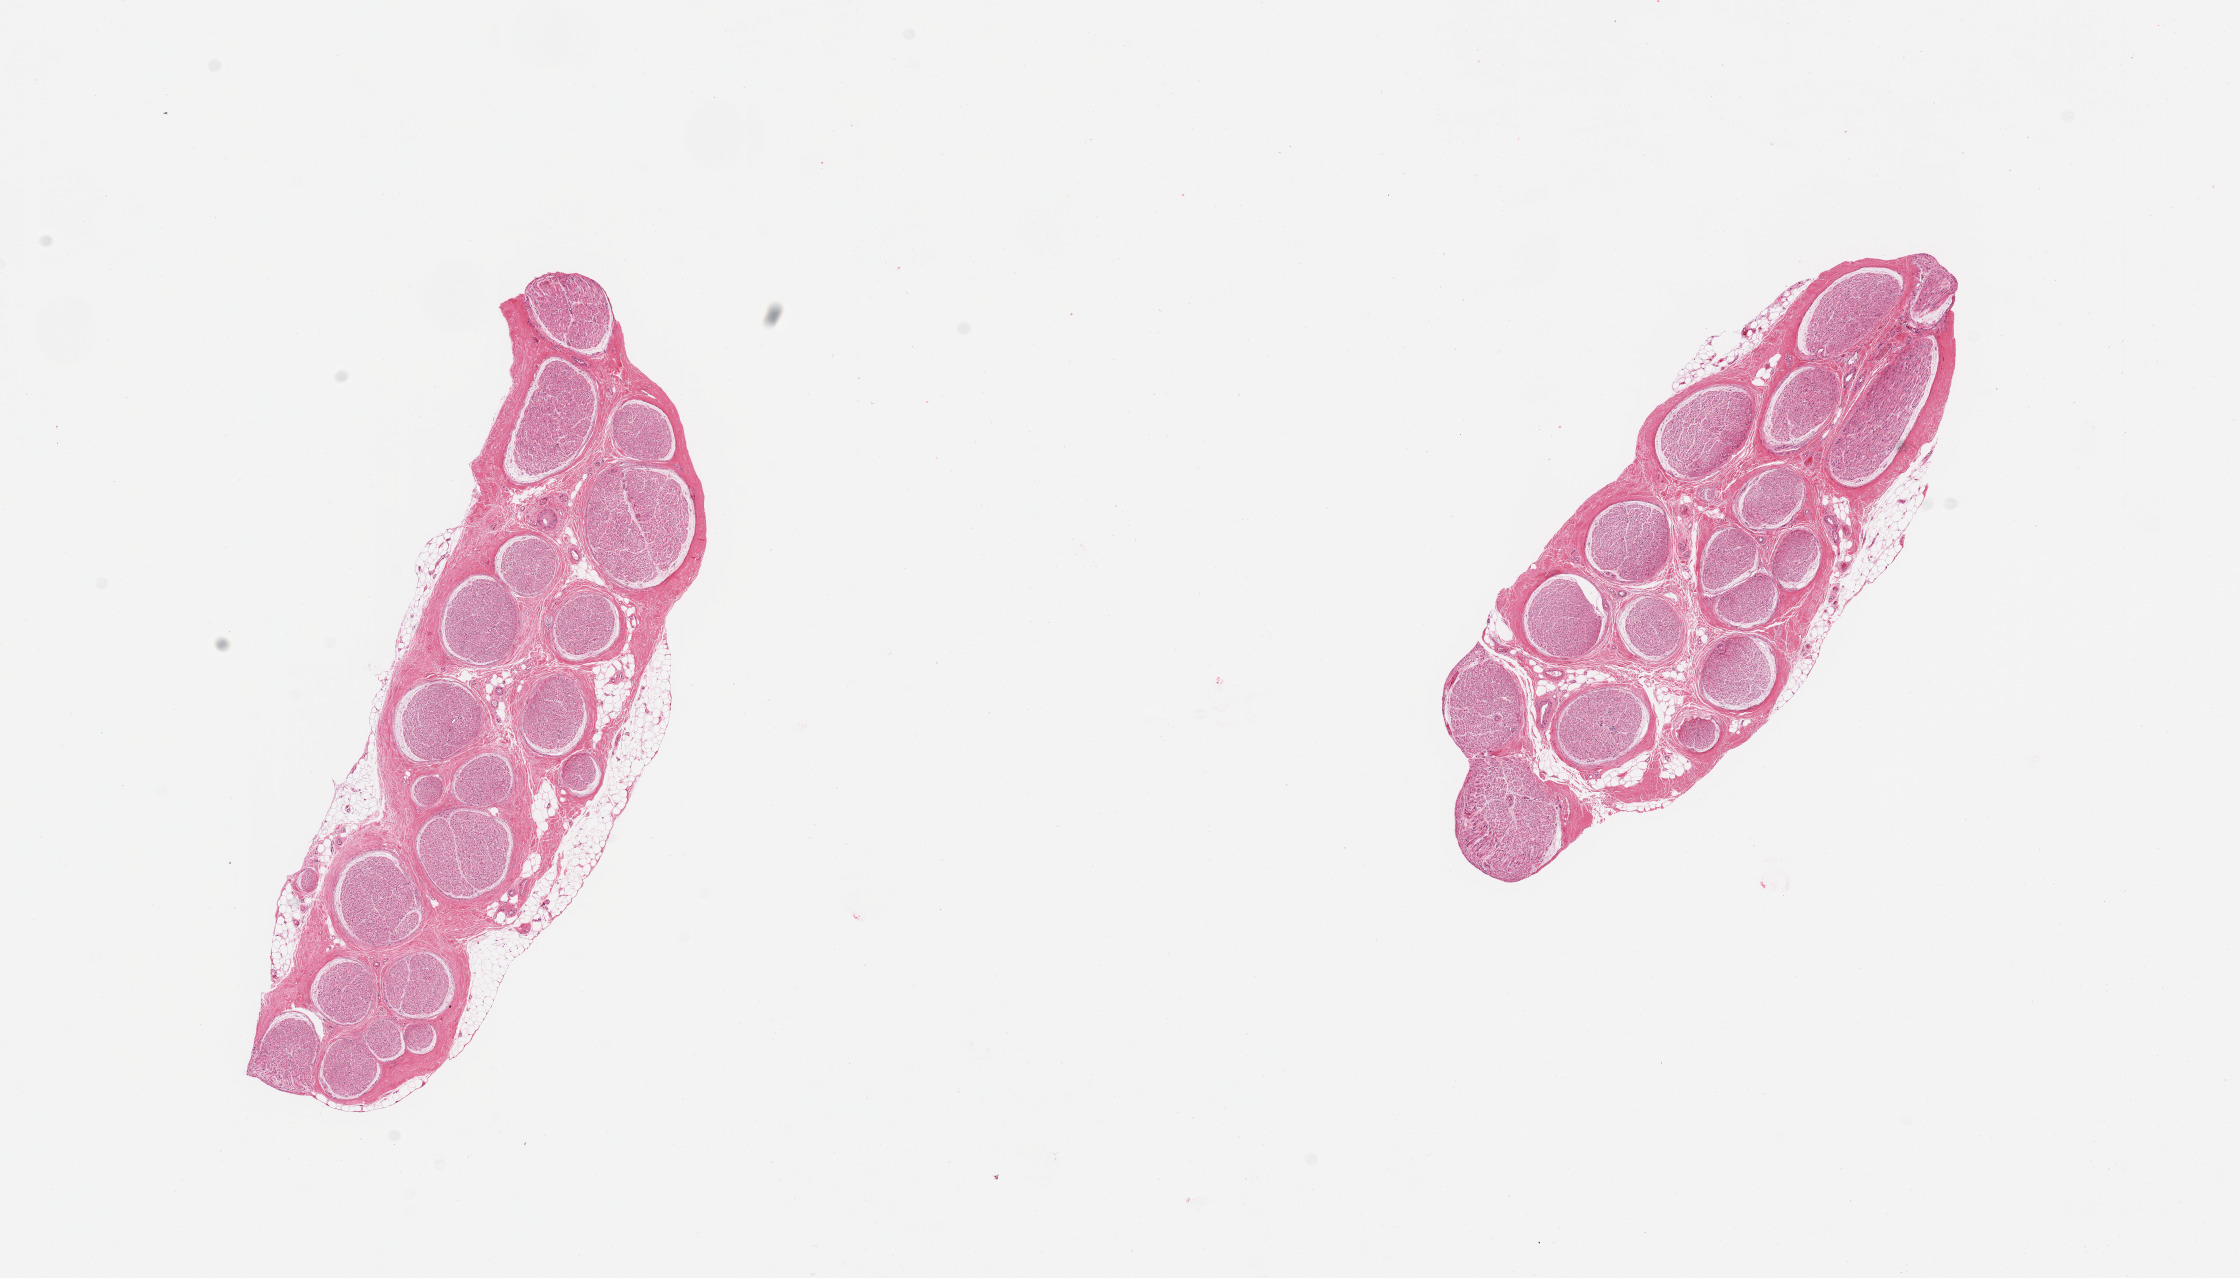
Whole-slide image, haematoxylin and eosin stain — whole scanned area (about 17.7 x 10.1 mm, slide scanned at 20x) shown as a low-resolution overview, PAXgene-fixed paraffin-embedded (PFPE) section, sampled site (target tissue): tibial nerve, tissue donor sample.
Review note (as recorded): 2 pieces; well trimmed; 10% external fat.